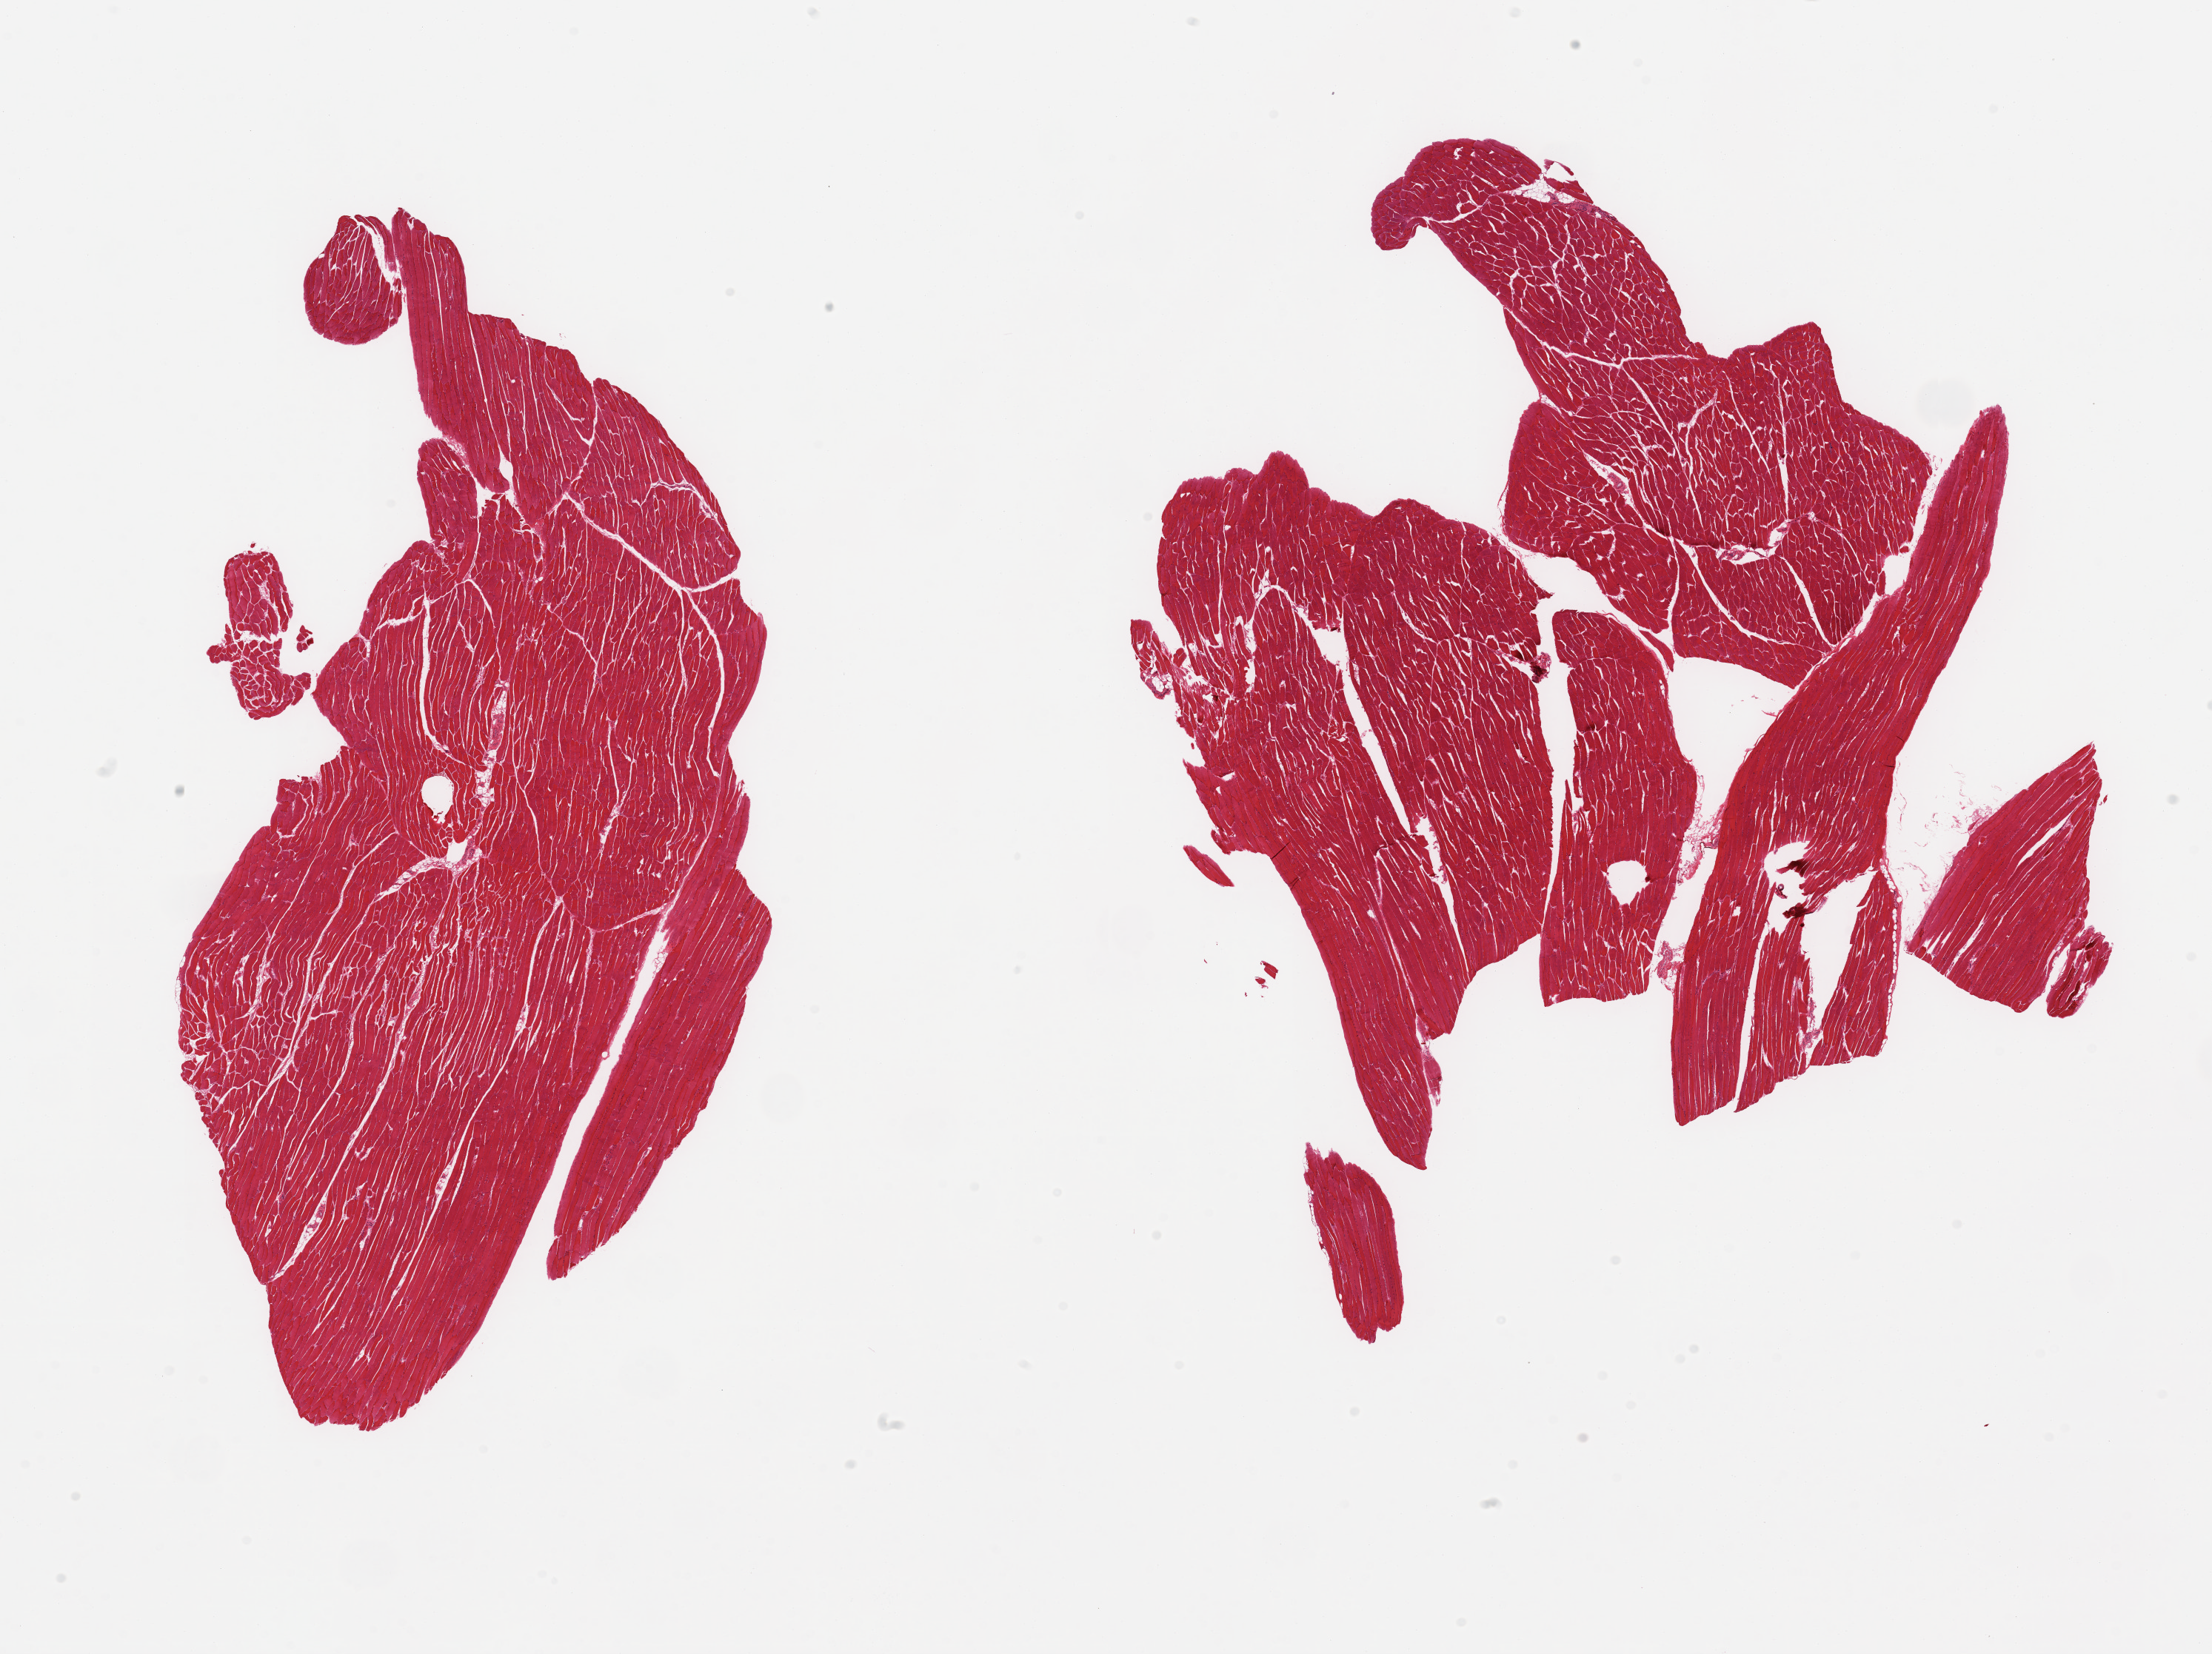
Whole-slide image, hematoxylin and eosin (H&E) stain, low-resolution overview of the scanned area, about 23.6 x 17.7 mm (acquisition: 20x scan); PAXgene-fixed paraffin-embedded (PFPE) section; sampled site (target tissue): skeletal muscle; donor tissue sample. Male donor.
Pathologist's review note for this sample: 2 pieces, trace interstitial fat.